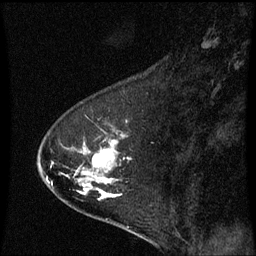
Breast MRI (dynamic contrast-enhanced), one sagittal slice; position 18 of 60 along the scan axis; dynamic contrast-enhanced series, image 2 of 3 at this slice position (ordered by acquisition); 1.5 T; TE 4.2 ms, TR 8.9 ms; 2 mm slice thickness; 256 × 256 image matrix, field of view 200 × 200 mm. Patient: female, 53 years. Case-level facts recorded for this patient, not image findings: setting: breast cancer imaged before/during neoadjuvant chemotherapy; receptor status: HR-positive, HER2-negative.
Outlined on this slice (semi-automatically segmented with operator editing):
- analysis volume of interest (the breast-tissue region the enhancement analysis was run in; not a lesion): bounding box (x1, y1, x2, y2) in pixels: (38, 120, 133, 221)
- tumour enhancement mask (voxels above the 70 % enhancement threshold inside the analysis volume of interest): (82, 142, 119, 197)